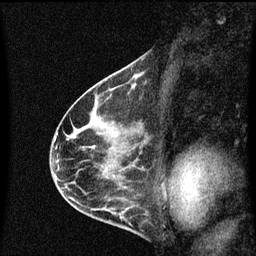
Breast MRI (dynamic contrast-enhanced), one sagittal slice. Slice 36 of 60 in the series (ordered by position). Dynamic contrast-enhanced series, image 2 of 3 at this slice position (ordered by acquisition). 1.5 T. TE 4.2 ms, TR 8.4 ms. 2 mm slice thickness. 256 × 256 image matrix, field of view 200 × 200 mm. Patient: female, 41 years.
Outlined on this slice (semi-automatically segmented with operator editing):
- analysis volume of interest (the breast-tissue region the enhancement analysis was run in; not a lesion): box from (x=121, y=74) to (x=145, y=99) px
- tumour enhancement mask (voxels above the 70 % enhancement threshold inside the analysis volume of interest): (x=133, y=76)–(x=135, y=79)